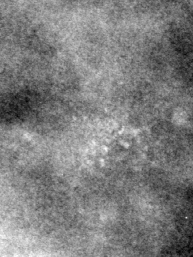
Cropped region of a digitized screen-film mammogram centred on a radiologist-marked abnormality; left breast; CC view.
- Finding: calcifications, morphology pleomorphic, distribution clustered; BI-RADS assessment category 4; subtlety rating 2 on a 1 (subtle) to 5 (obvious) scale; pathology (as recorded): benign.